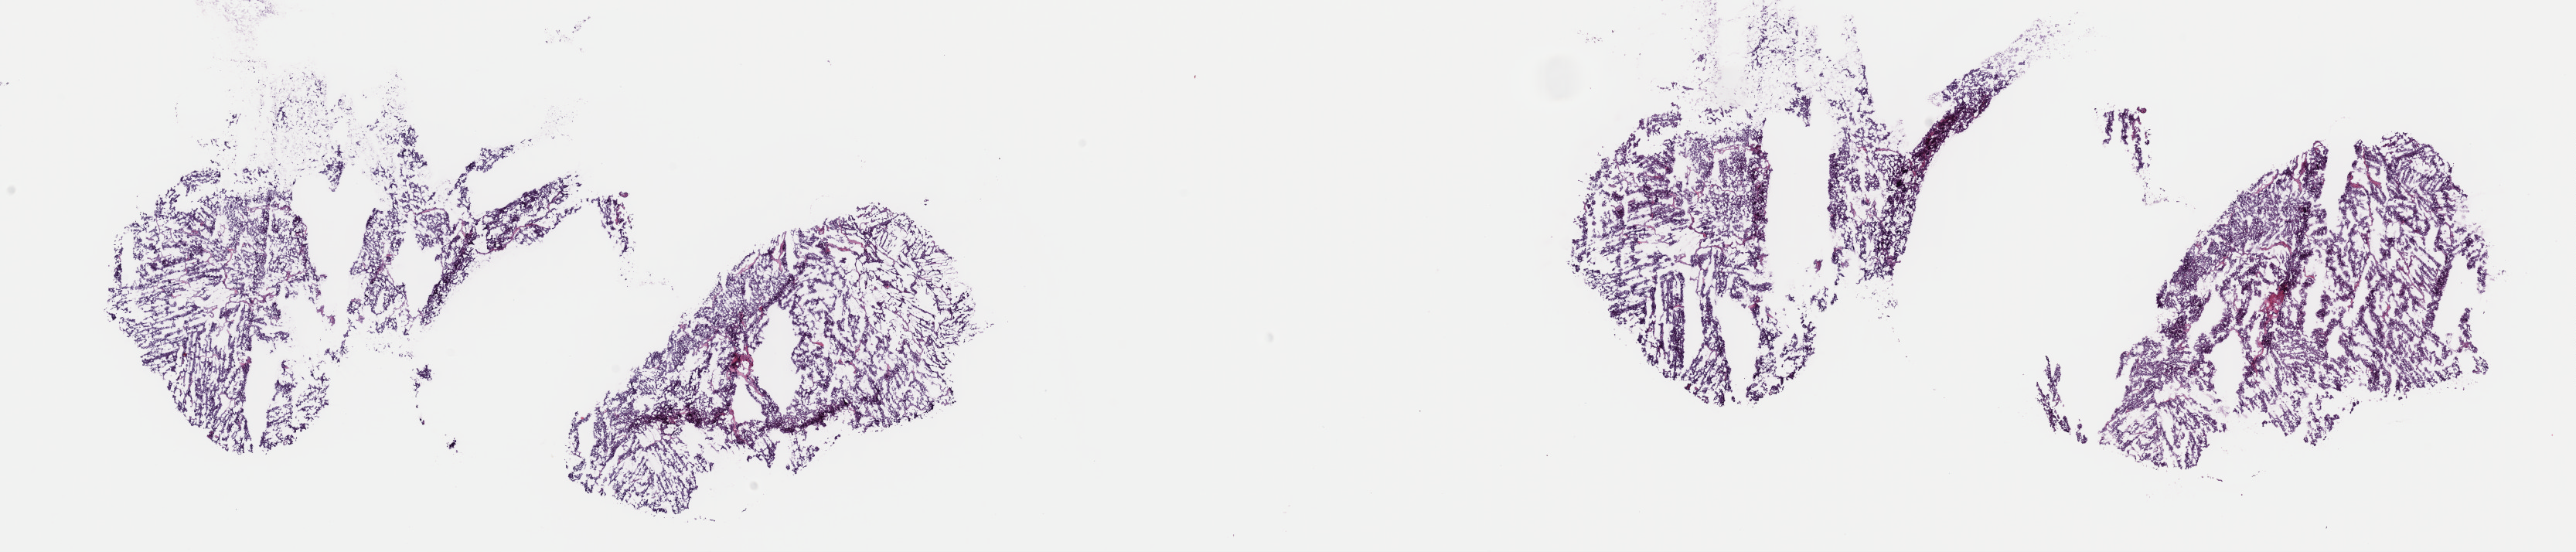
Whole-slide histology image, H&E, whole scanned area (about 26.3 x 5.6 mm) shown as a low-resolution overview. Frozen section from the top of the tissue portion. Adrenal gland, primary tumour sample. Male patient; age at initial diagnosis 61 years. Slide review estimates, as recorded: tumour cells 90%, tumour nuclei 100%, normal cells 0%, stromal cells 10%, necrosis 0%. Infiltration values recorded for this section: lymphocyte infiltration 0%, monocyte infiltration 0%, neutrophil infiltration 0%.
Diagnosis: Pheochromocytoma, NOS.